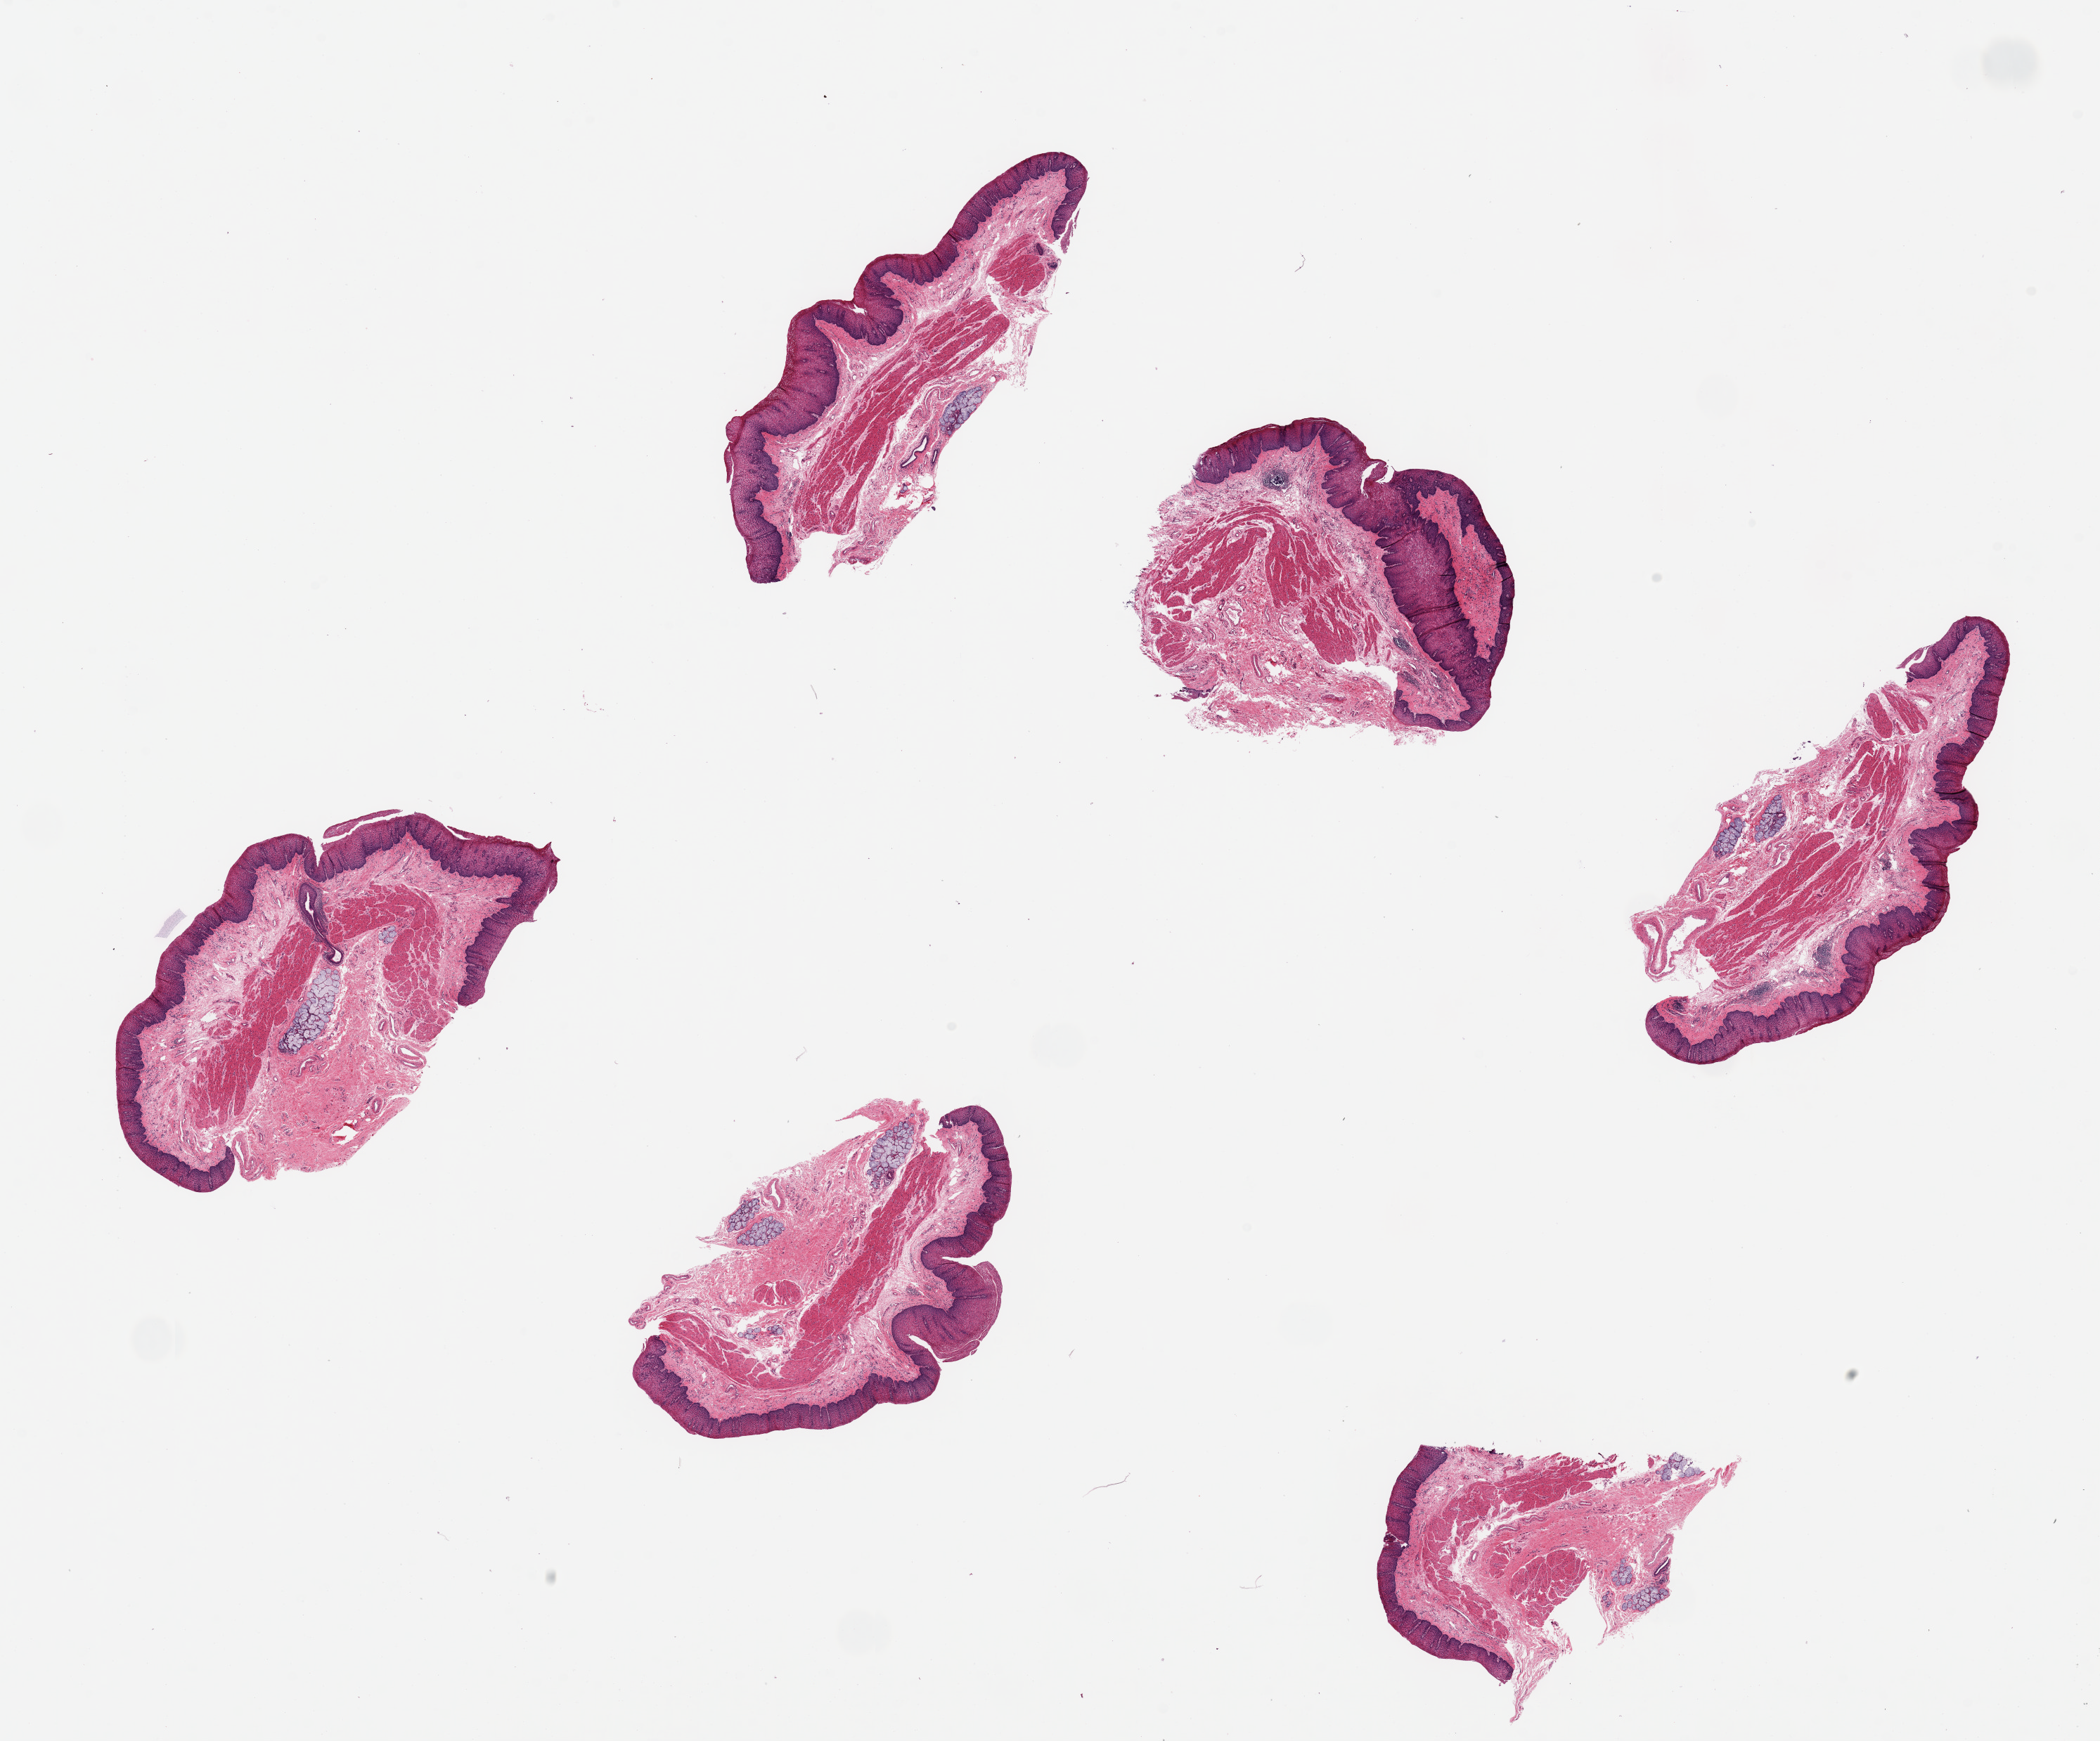
Digitized hematoxylin and eosin (H&E)-stained section, brightfield, whole scanned area (about 23.6 x 19.6 mm, acquisition: 20x scan) shown as a low-resolution overview. PAXgene-fixed paraffin-embedded (PFPE) section. Target tissue: esophageal mucous membrane. Tissue donor sample. Donor sex: male.
* pathologist's review note for this sample: 6 pieces ~7x2.5mm ~10 thickness is squamous mucosa, well preserved